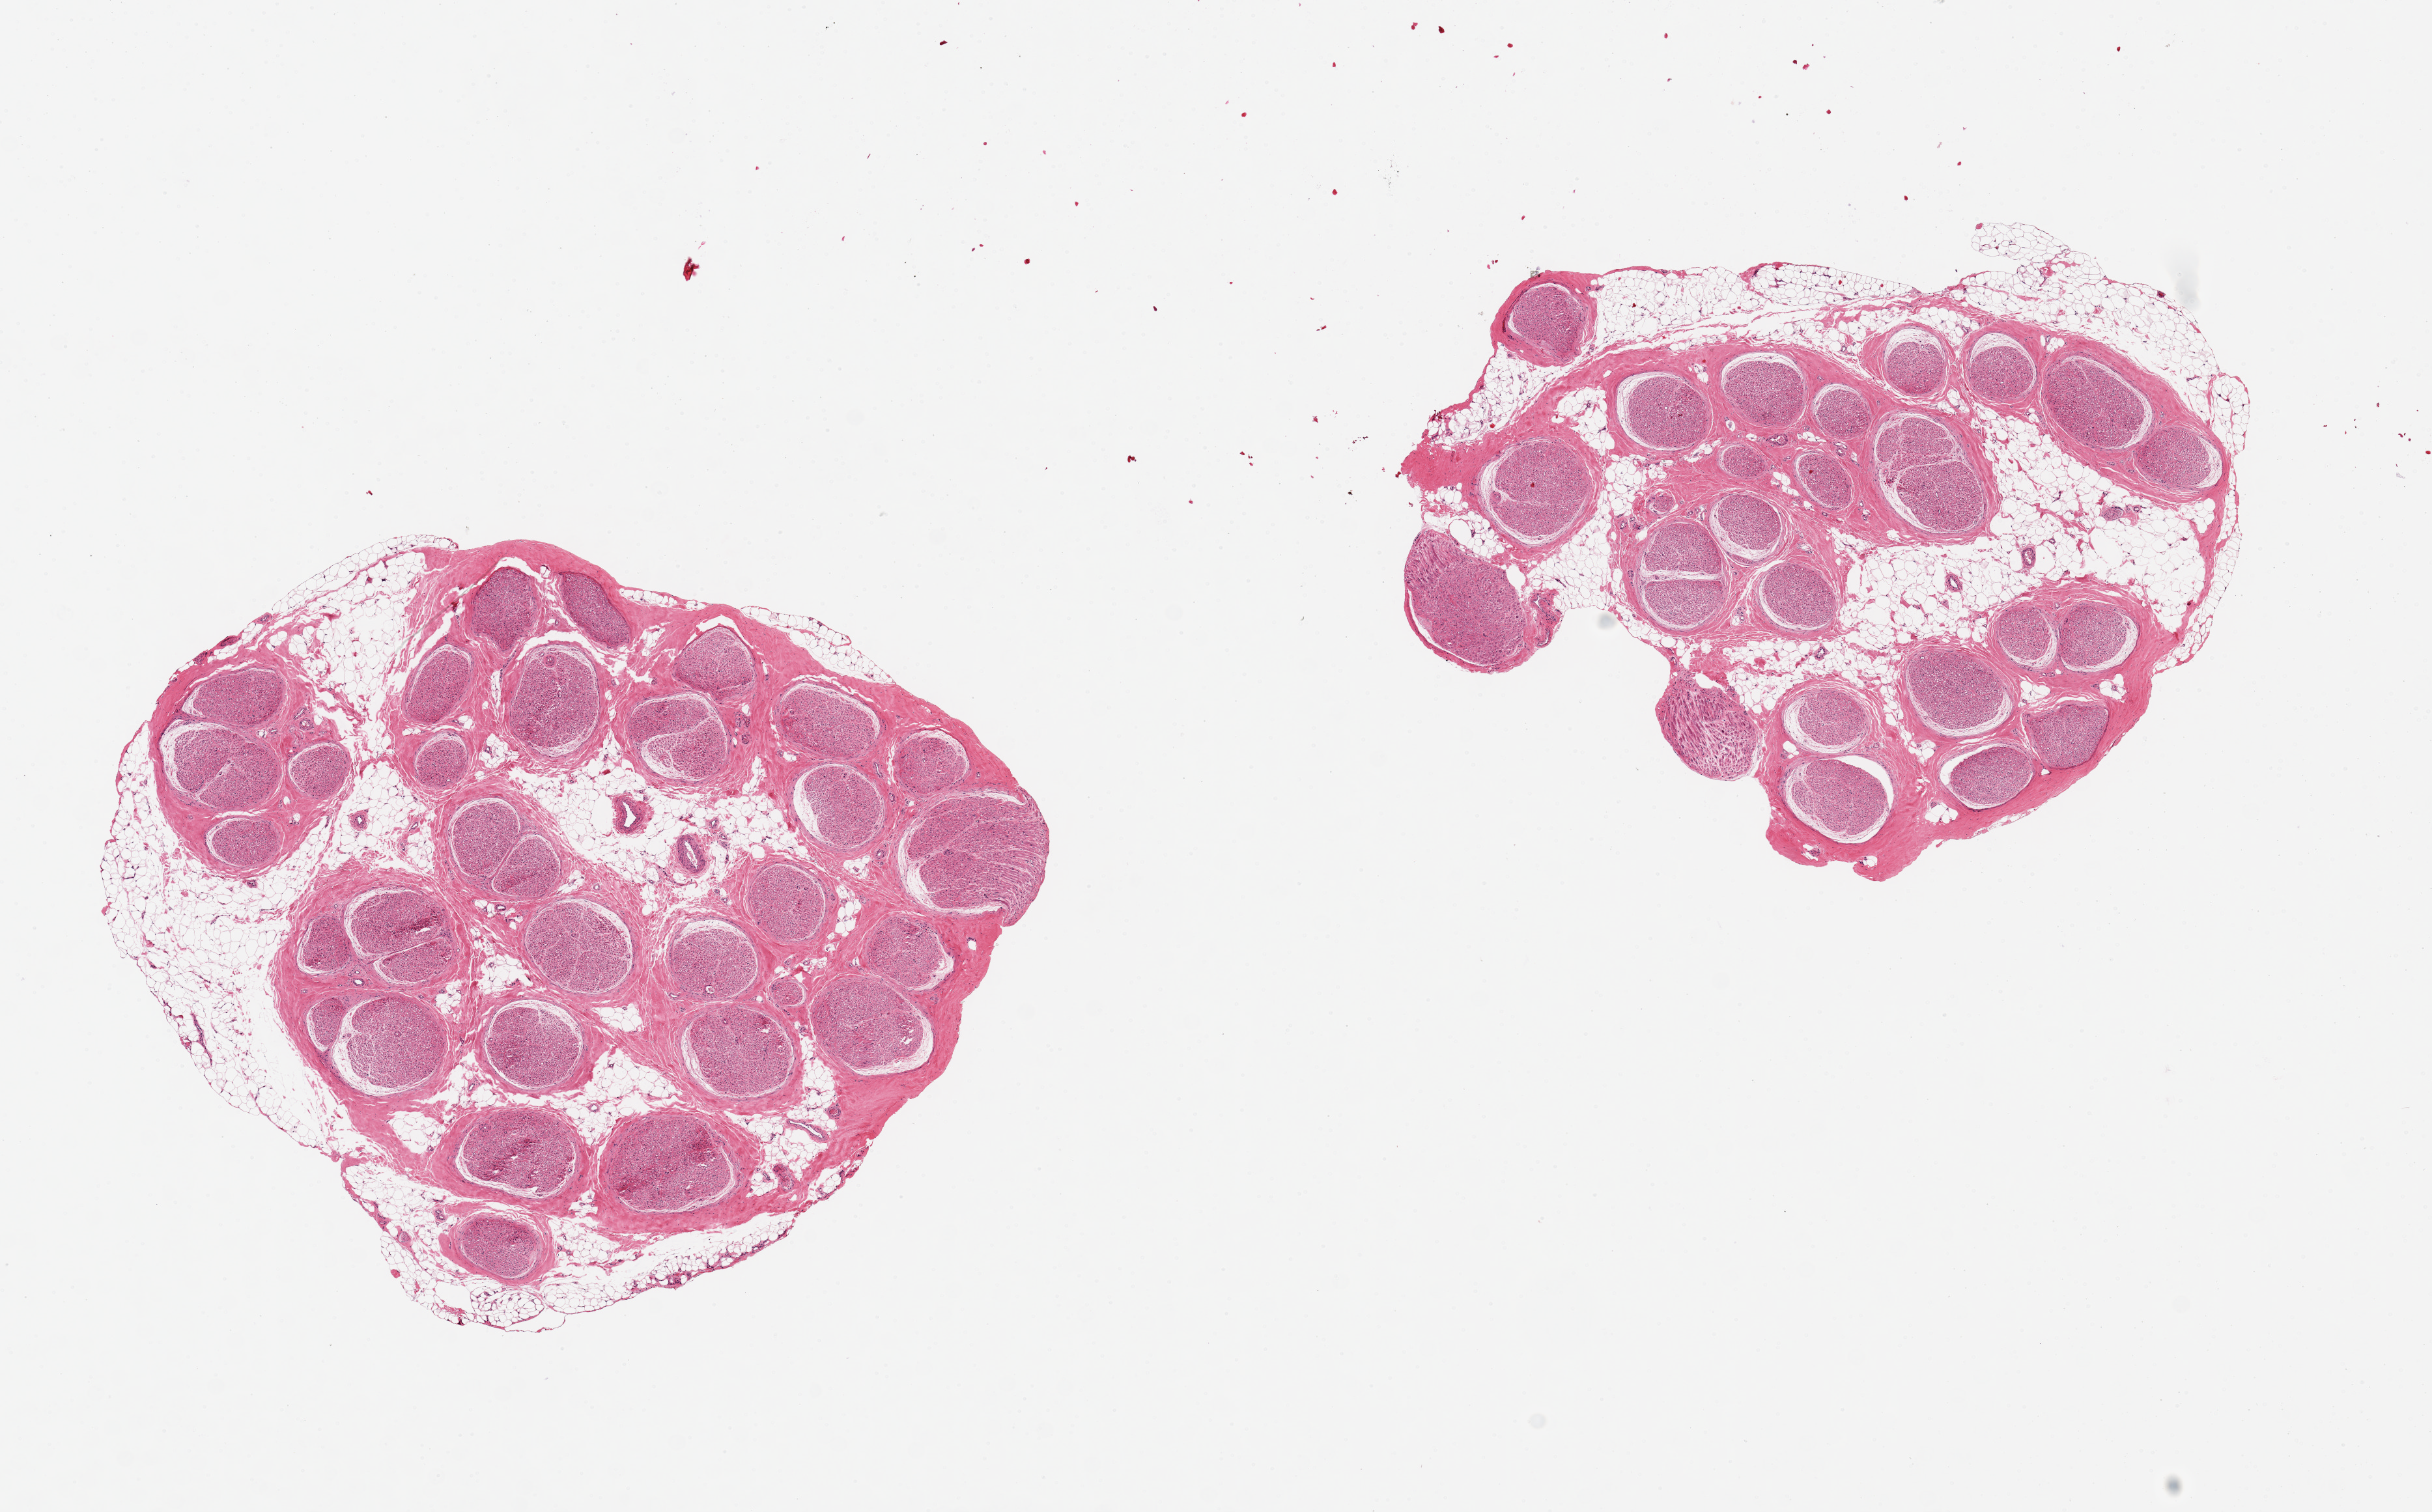
Whole-slide image, hematoxylin and eosin (H&E) stain — low-resolution overview of the scanned area, about 14.8 x 9.2 mm (slide scanned at 20x), PAXgene-fixed, paraffin-embedded tissue, sampled site (target tissue): tibial nerve, tissue donor sample. Donor sex: male.
Reviewer comment on this tissue sample: 2 aliquots, ~4mm d. Rim of fat from ~0.3-0.5mm thickness, discontinuous, around both.